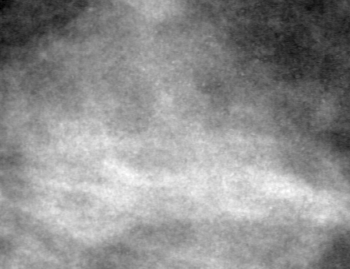
Cropped region of a digitized screen-film mammogram centred on a radiologist-marked abnormality; right breast; CC view.
Mass, shape lobulated, margins ill defined; BI-RADS assessment category 4; subtlety rating 2 on a 1 (subtle) to 5 (obvious) scale; pathology result (as recorded, not read from the image): benign.